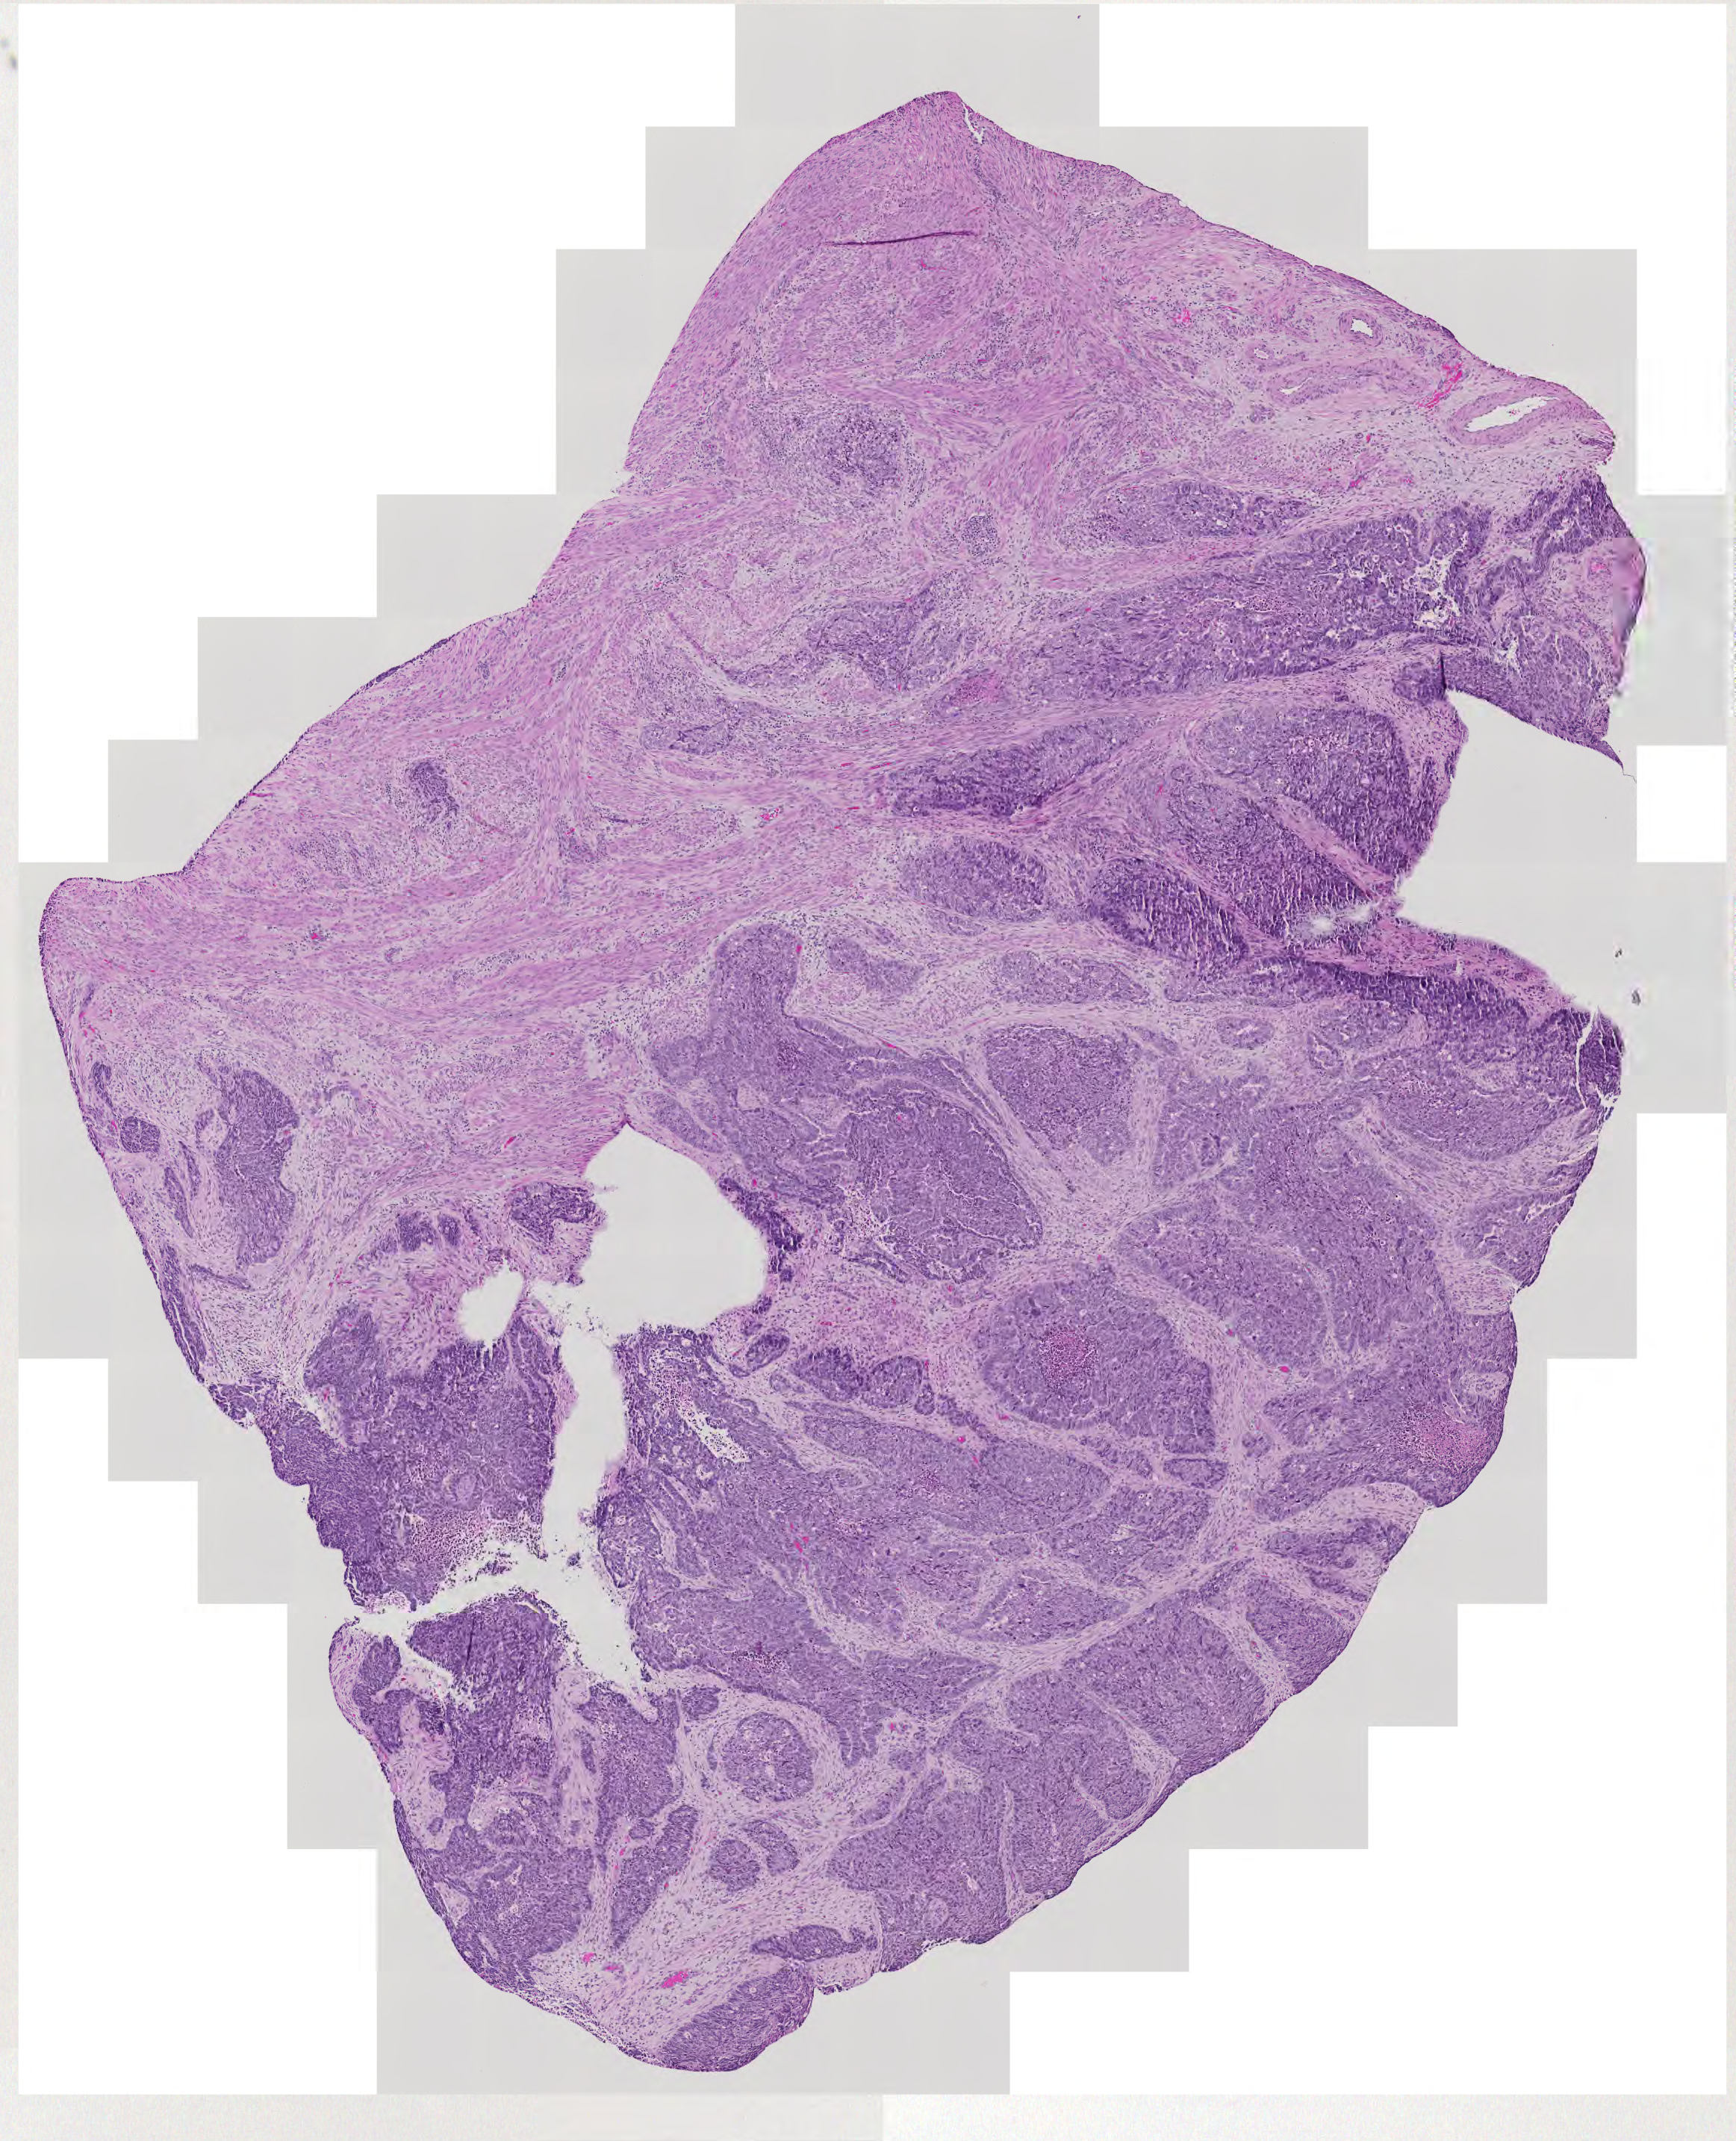
Whole-slide histology image, Hematoxylin and eosin (H&E) stained — shown as a low-resolution overview of the whole scanned area (about 6.0 x 7.4 mm, acquisition: 20x scan). Uterus, tumour tissue. 65-year-old female patient. Histologic grade: G3 (poorly differentiated).
• histologic diagnosis: Endometrioid adenocarcinoma, NOS
• AJCC pathologic stage: IV